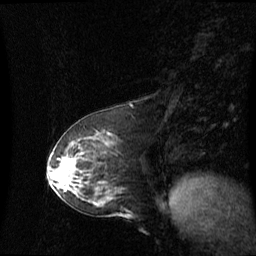
Breast MRI (dynamic contrast-enhanced), one sagittal slice; position 27 of 60 along the scan axis; dynamic contrast-enhanced series, image 2 of 3 at this slice position (ordered by acquisition); 1.5 T; TE 4.2 ms, TR 8.4 ms; 2.1 mm slice thickness; 256 × 256 image matrix, field of view 260 × 260 mm. Female patient, age 59 years. From the clinical record (not read from this slice): setting: breast cancer imaged before/during neoadjuvant chemotherapy; receptor status: HR-positive, HER2-negative.
Outlined on this slice (semi-automatically segmented with operator editing):
- analysis volume of interest (the breast-tissue region the enhancement analysis was run in; not a lesion): bounding box (x1, y1, x2, y2) in pixels: (55, 149, 88, 191)
- tumour enhancement mask (voxels above the 70 % enhancement threshold inside the analysis volume of interest): (63, 161, 76, 171)